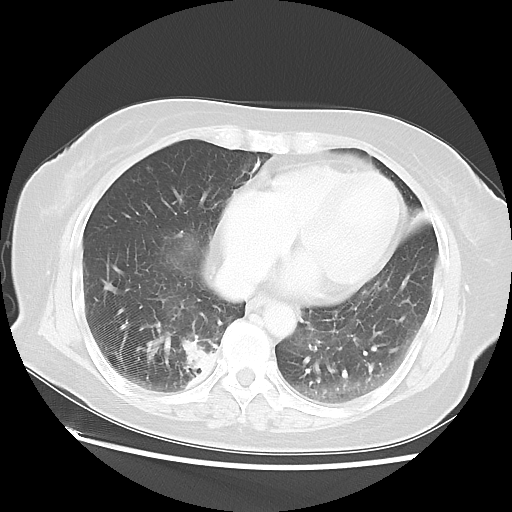
Chest CT, one axial slice. Position 20 of 52 along the scan axis. Reconstruction kernel LUNG. 120 kVp. Lung window (W 1500 / L -600 HU). 512 × 512 image matrix. Patient: female, 69 years. Case-level facts recorded for this patient, not image findings: clinical TNM (as recorded): T2 N1 M1a.
Outlined on this slice (rectangle marked by the reading radiologist):
- lung tumour (recorded histology: adenocarcinoma): box from (x=170, y=332) to (x=220, y=391) px